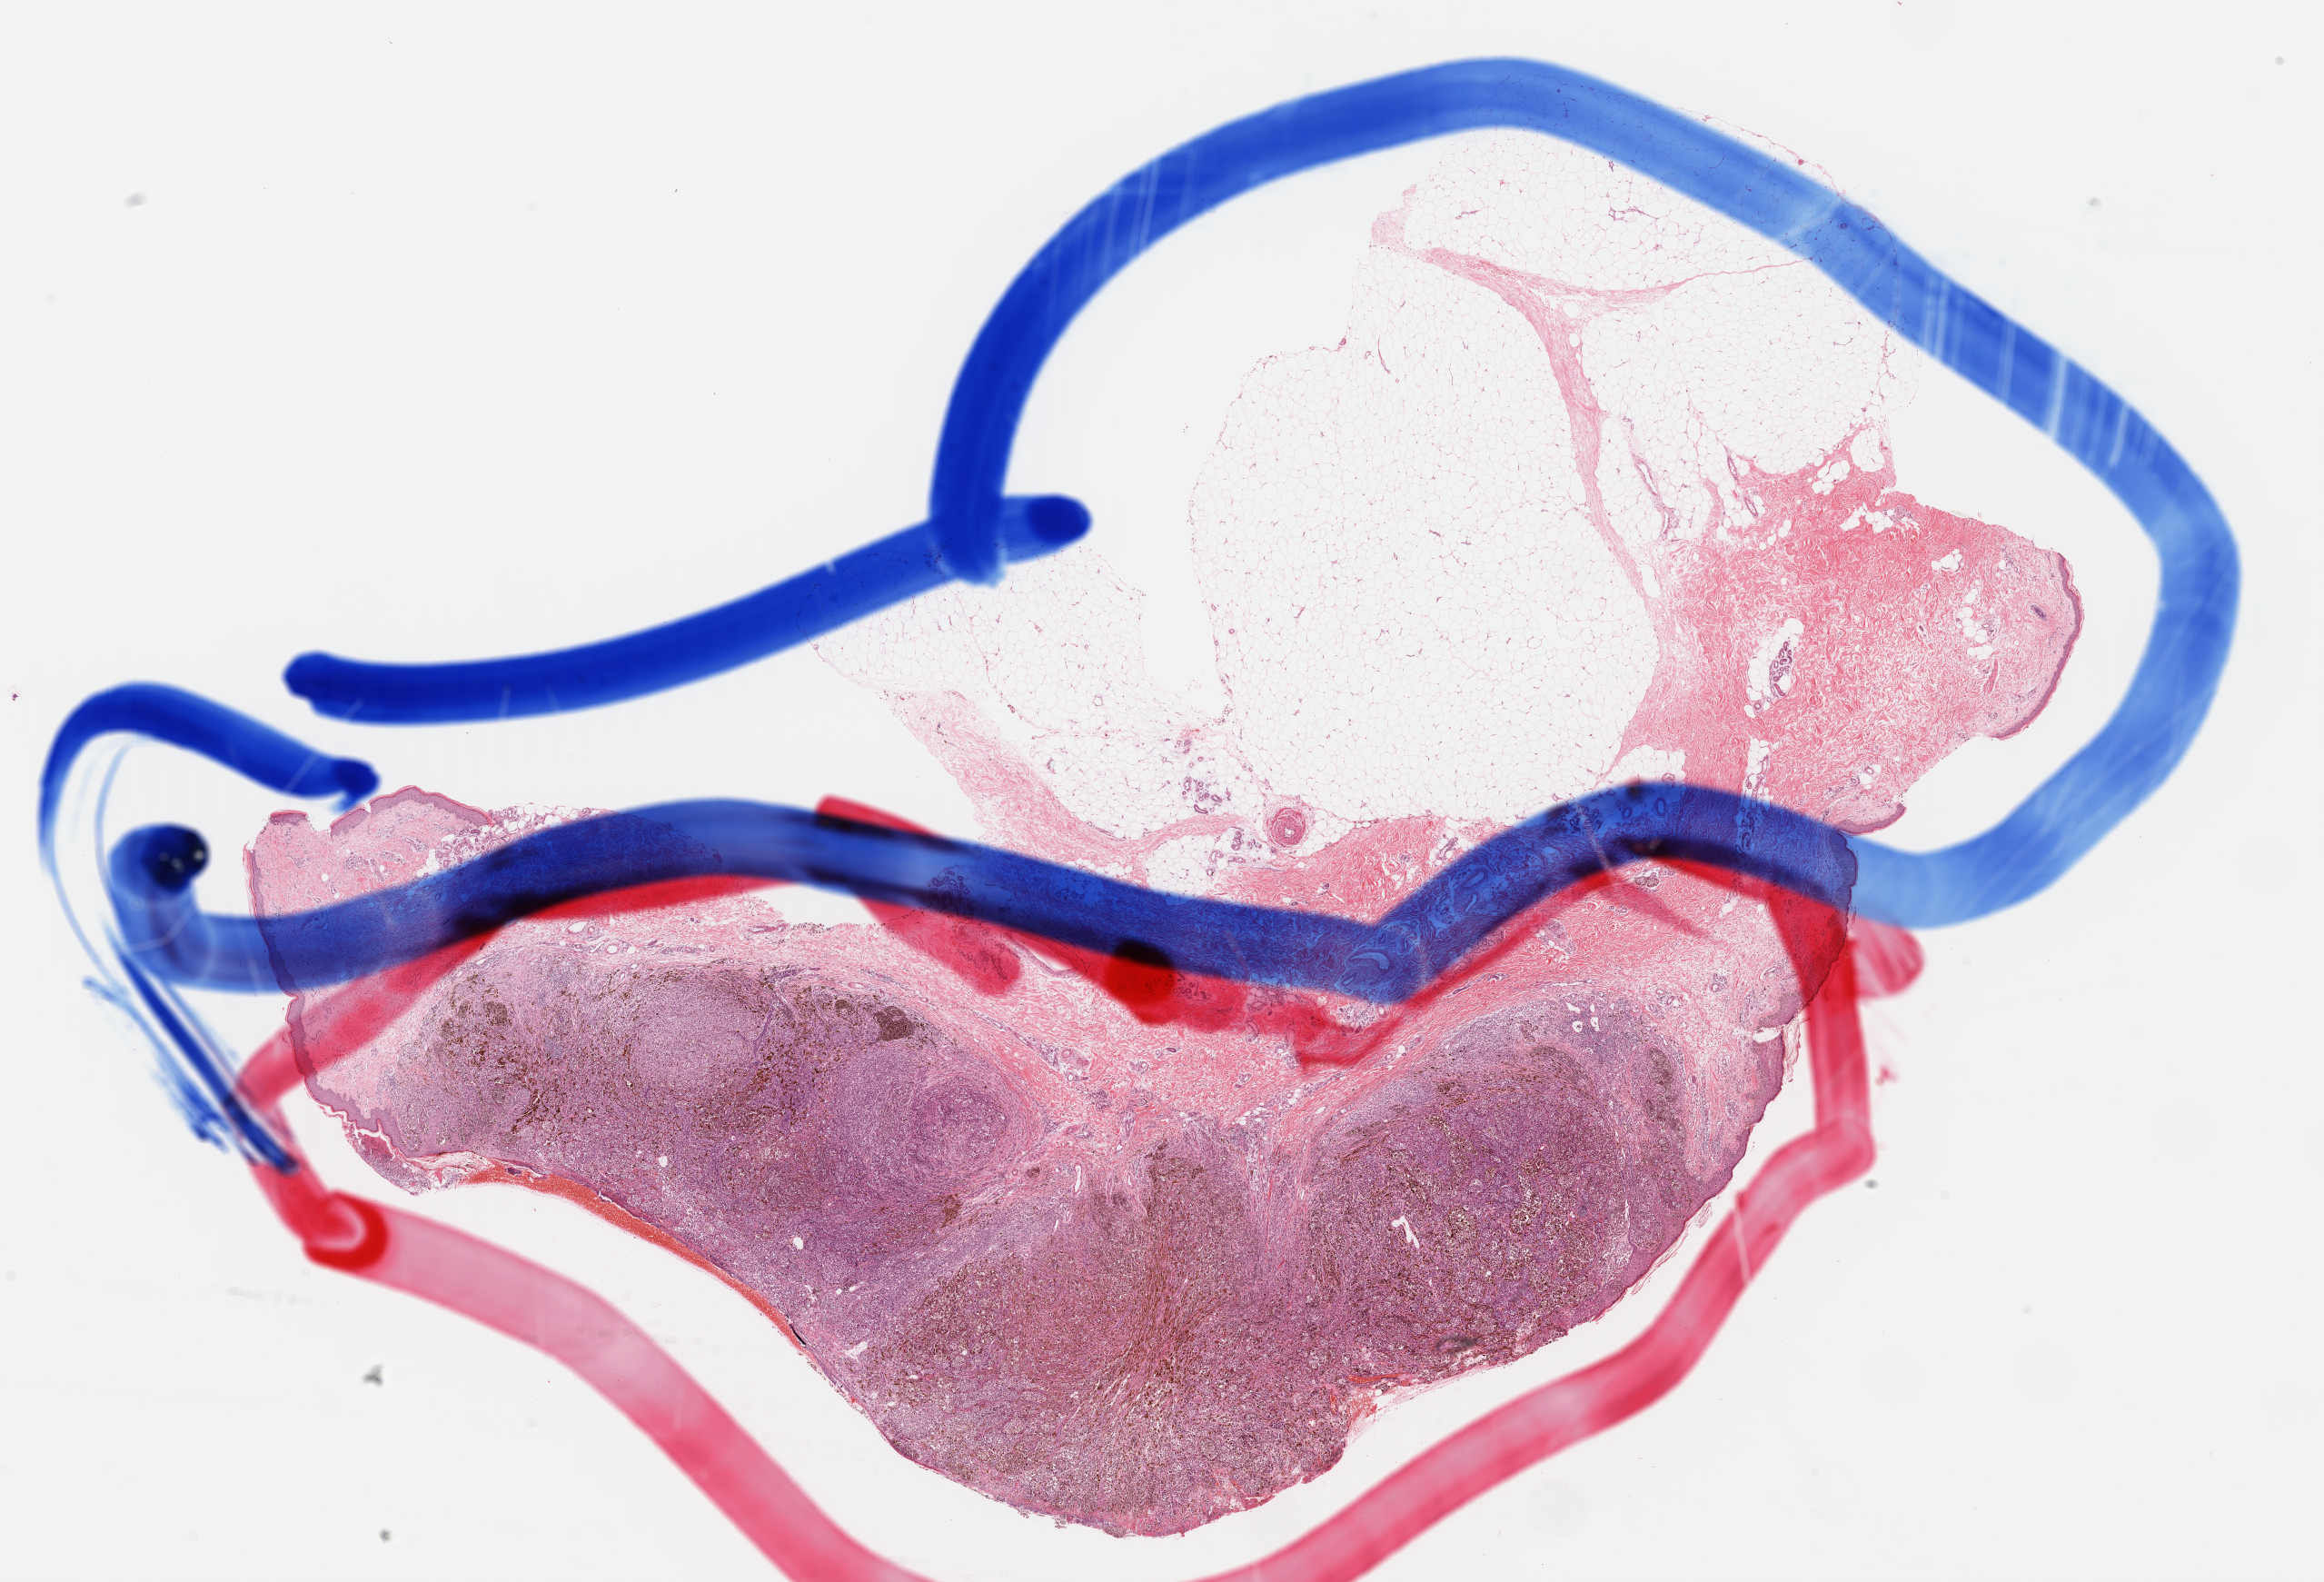
Digitized H&E tissue section (whole slide), whole scanned area (about 20.2 x 13.7 mm, acquisition: 40x scan) shown as a low-resolution overview, FFPE section, sample: primary tumour, skin. Patient: female, age at initial diagnosis 76 years.
AJCC pathologic stage: IIA (7th edition). Histologic diagnosis: Malignant melanoma, NOS. TNM: T3a N0 M0.